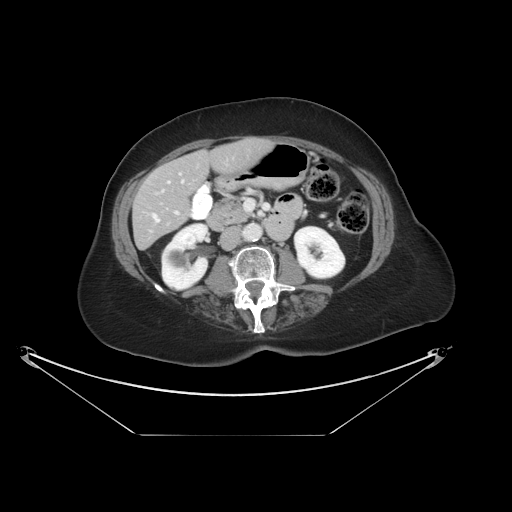
Contrast-enhanced abdominal CT, one axial slice. Position 12 of 36 along the scan axis. Reconstruction kernel STANDARD. 120 kVp. Intravenous contrast given. Soft-tissue window (W 400 / L 40 HU). 5 mm slice thickness. 512 × 512 image matrix. Female patient, age 70 years. Case-level facts recorded for this patient, not image findings: diagnosis: colorectal cancer liver metastases, imaged before liver resection.
Outlined on this slice (manually delineated by an expert):
- hepatic veins: box from (x=153, y=180) to (x=184, y=222) px
- liver: (x=134, y=140)–(x=268, y=248)
- planned liver remnant (the part of the liver to remain after resection): (x=134, y=140)–(x=268, y=248)
- portal vein (with intrahepatic branches): (x=162, y=191)–(x=179, y=215)